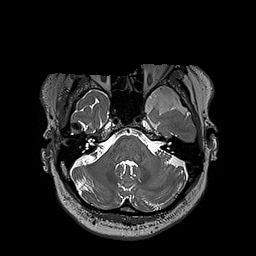
Brain MRI from a brain-tumour surgery series, one axial slice; slice 150 of 192 in the series (ordered by position); 256 × 256 image matrix, field of view 250 × 250 mm. From the clinical record (not read from this slice): histopathology: Oligodendroglioma; WHO grade: 3.
Outlined on this slice (expert manual segmentation):
- tumour: bounding box [x1, y1, x2, y2] px = [124, 85, 197, 112]